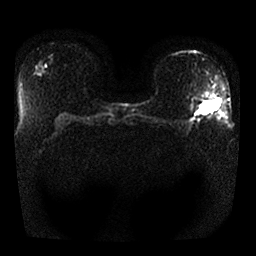
Breast MRI, one axial slice. Slice 16 of 25 in the series (ordered by position). Diffusion-weighted series; image 2 of 4 stored at this slice position (different b-values; order by instance number). 1.5 T. 4 mm slice thickness. 256 × 256 image matrix, field of view 340 × 340 mm. Female patient.
Structures marked on this image (manually delineated by an expert):
- tumour on diffusion-weighted imaging: bounding box (x1, y1, x2, y2) in pixels: (199, 102, 218, 114)